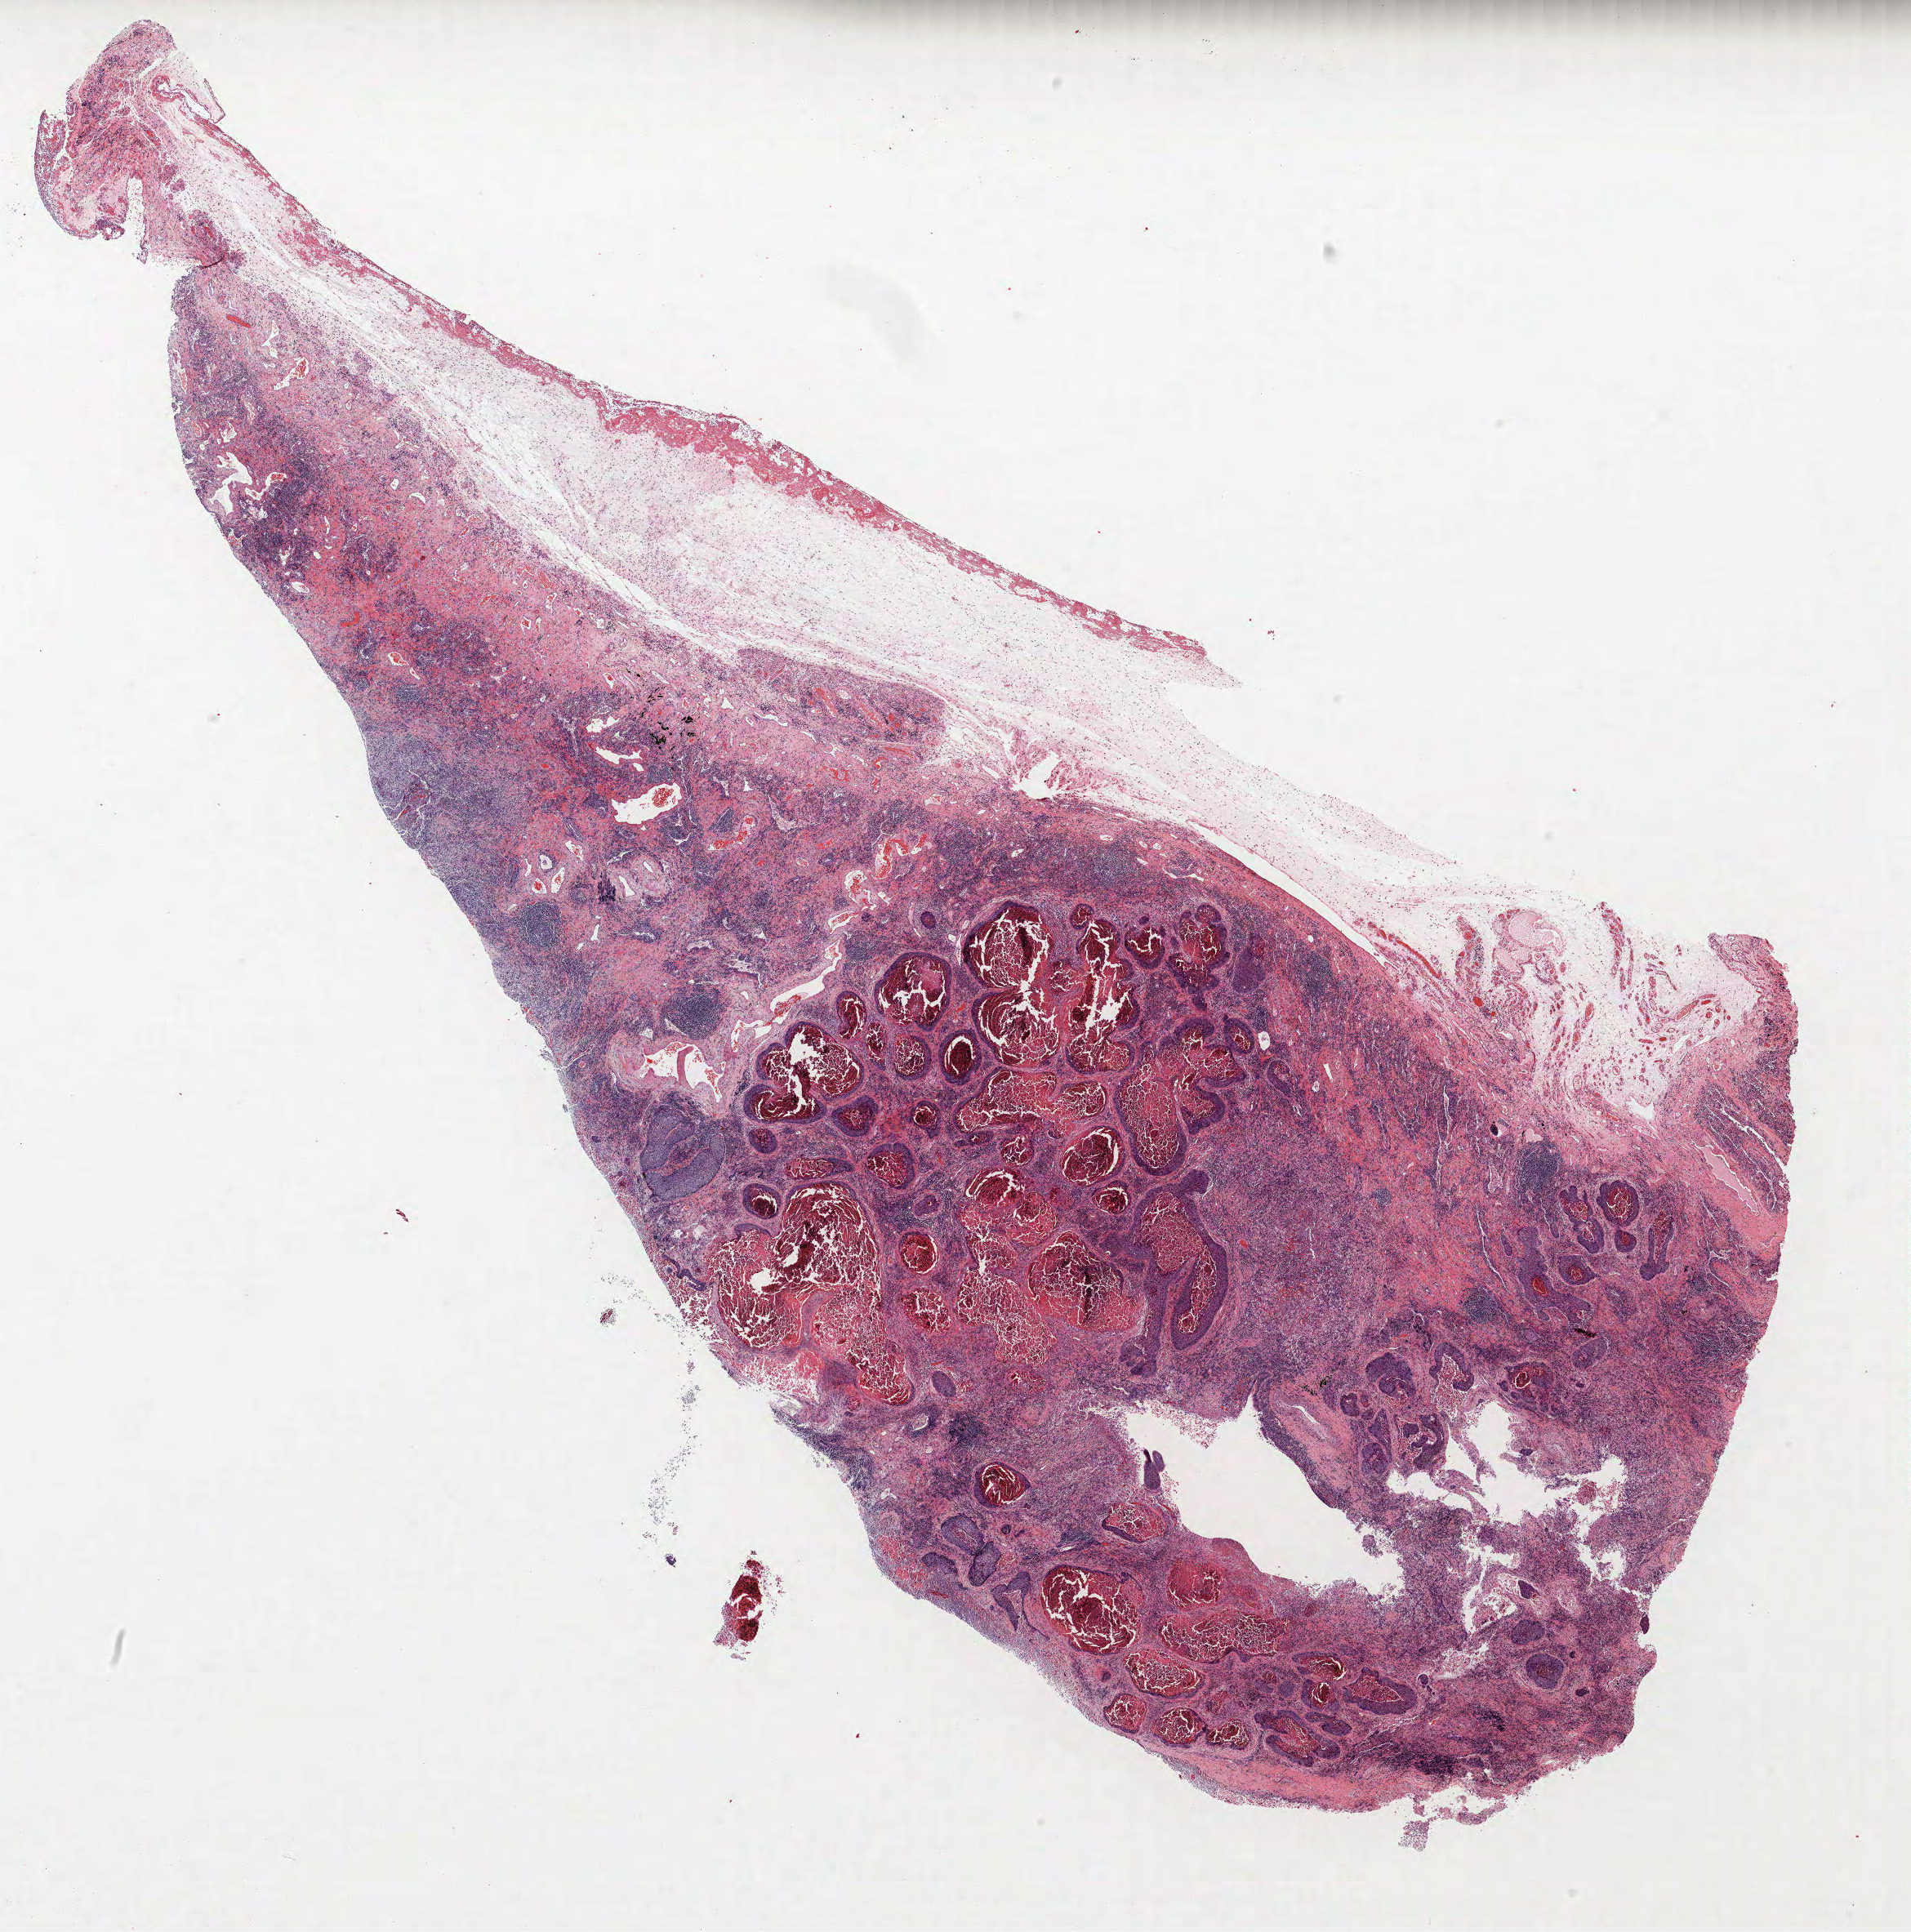
H&E whole-slide image, whole scanned area (about 18.7 x 18.9 mm, acquisition: 40x scan) shown as a low-resolution overview; formalin-fixed paraffin-embedded (FFPE) section; lung tissue. Male, age 74 at enrolment. Grade: poorly differentiated (G3).
ICD-O-3 topography: lower lobe of lung (C34.3). Primary tumour location (clinical record): right lower lobe. Stage (AJCC 6th edition): IIB. Tumour size (pathology): 80 mm. Participant's lung-cancer diagnosis: Squamous cell carcinoma, NOS (ICD-O-3 8070/3).